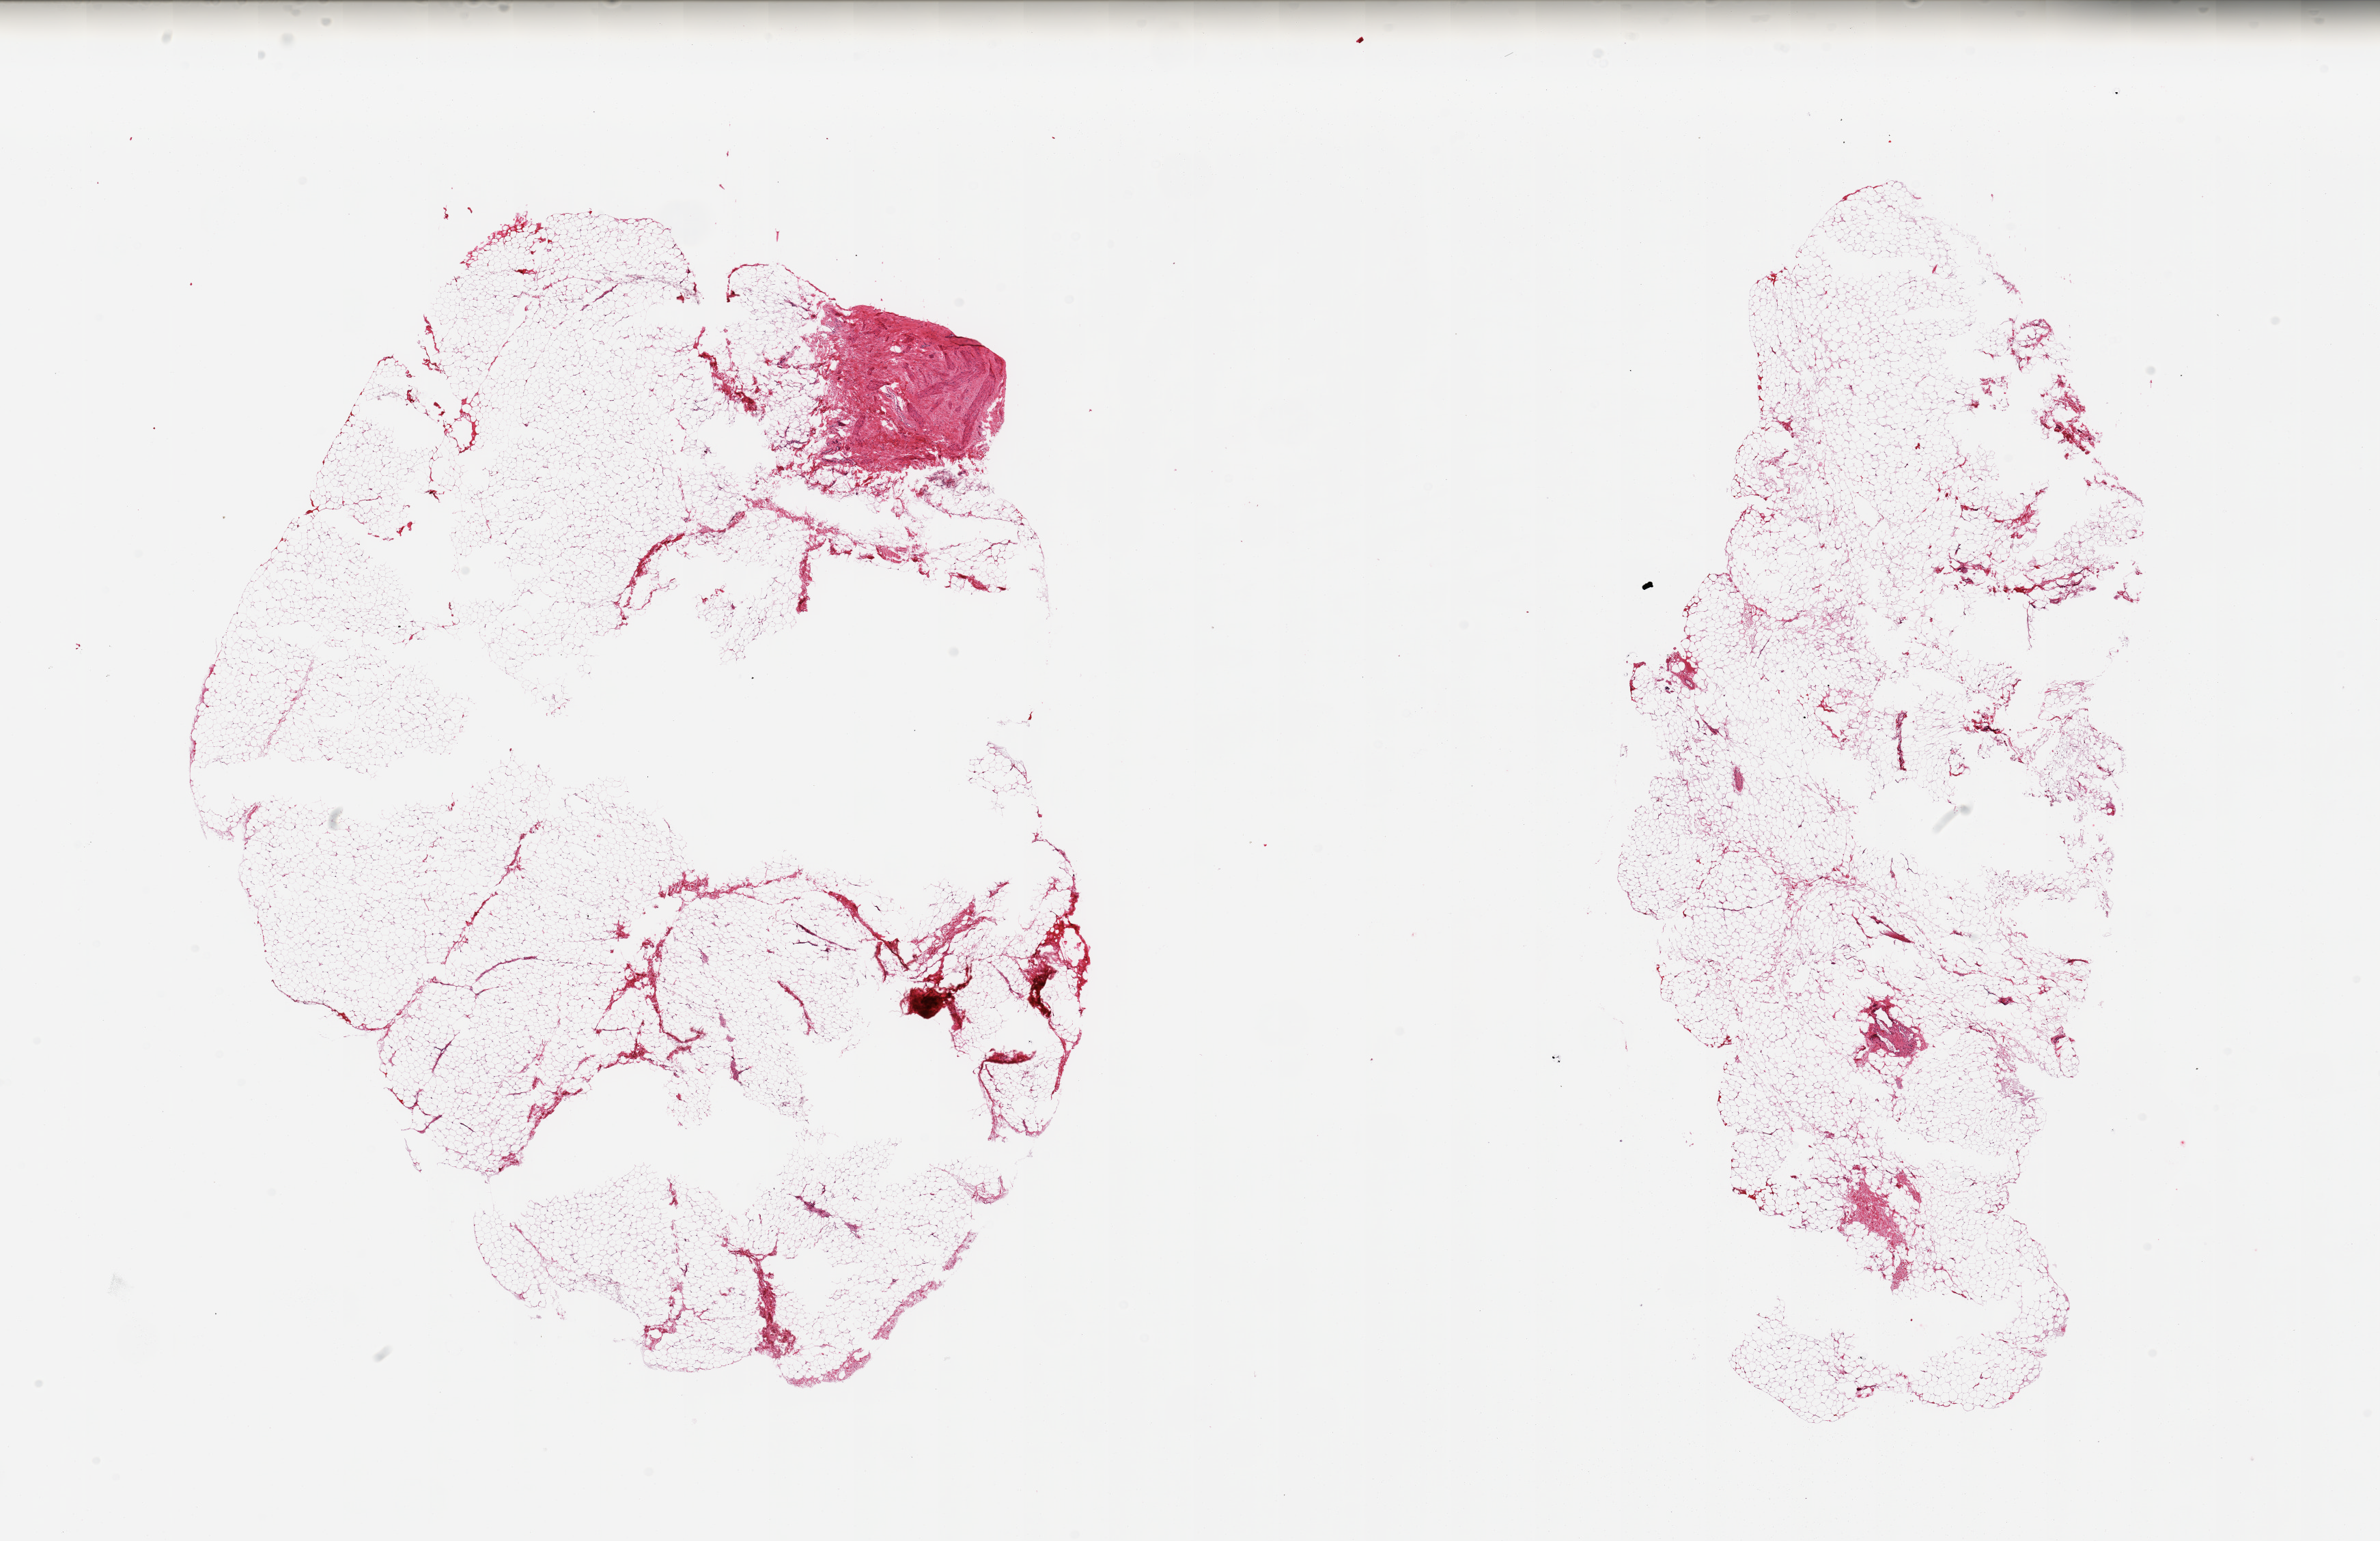
Whole-slide image, hematoxylin and eosin (H&E) stain, a low-resolution overview of the entire scanned area, about 27.6 x 17.9 mm (acquisition: 20x scan). PAXgene-fixed paraffin-embedded (PFPE) section. Section of prostate (target tissue). Donor tissue sample.
Reviewer comment on this tissue sample: 2 pieces, adipose tissue, unknown provenance.